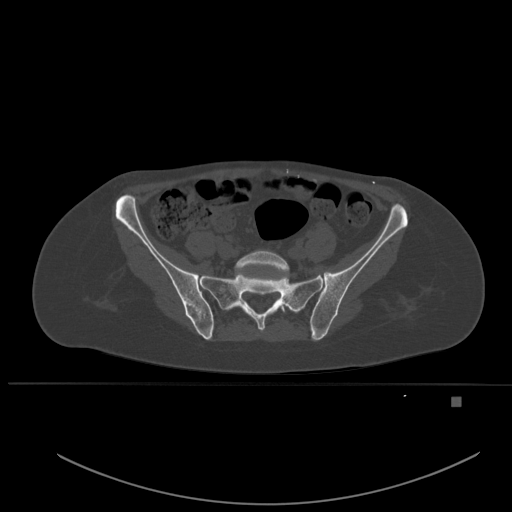
CT including the spine, one axial slice; position 141 of 651 along the scan axis; bone window (W 1800 / L 400 HU); 1.5 mm slice thickness; 512 × 512 image matrix, field of view 443 × 443 mm. Patient: female, 49 years. From the clinical record (not read from this slice): primary cancer: breast; vertebrae with lytic lesions (as recorded): L3, T12, L4.
Outlined on this slice (semi-automatically segmented with operator editing):
- L5 vertebra: bounding box (x1, y1, x2, y2) in pixels: (231, 251, 290, 312)